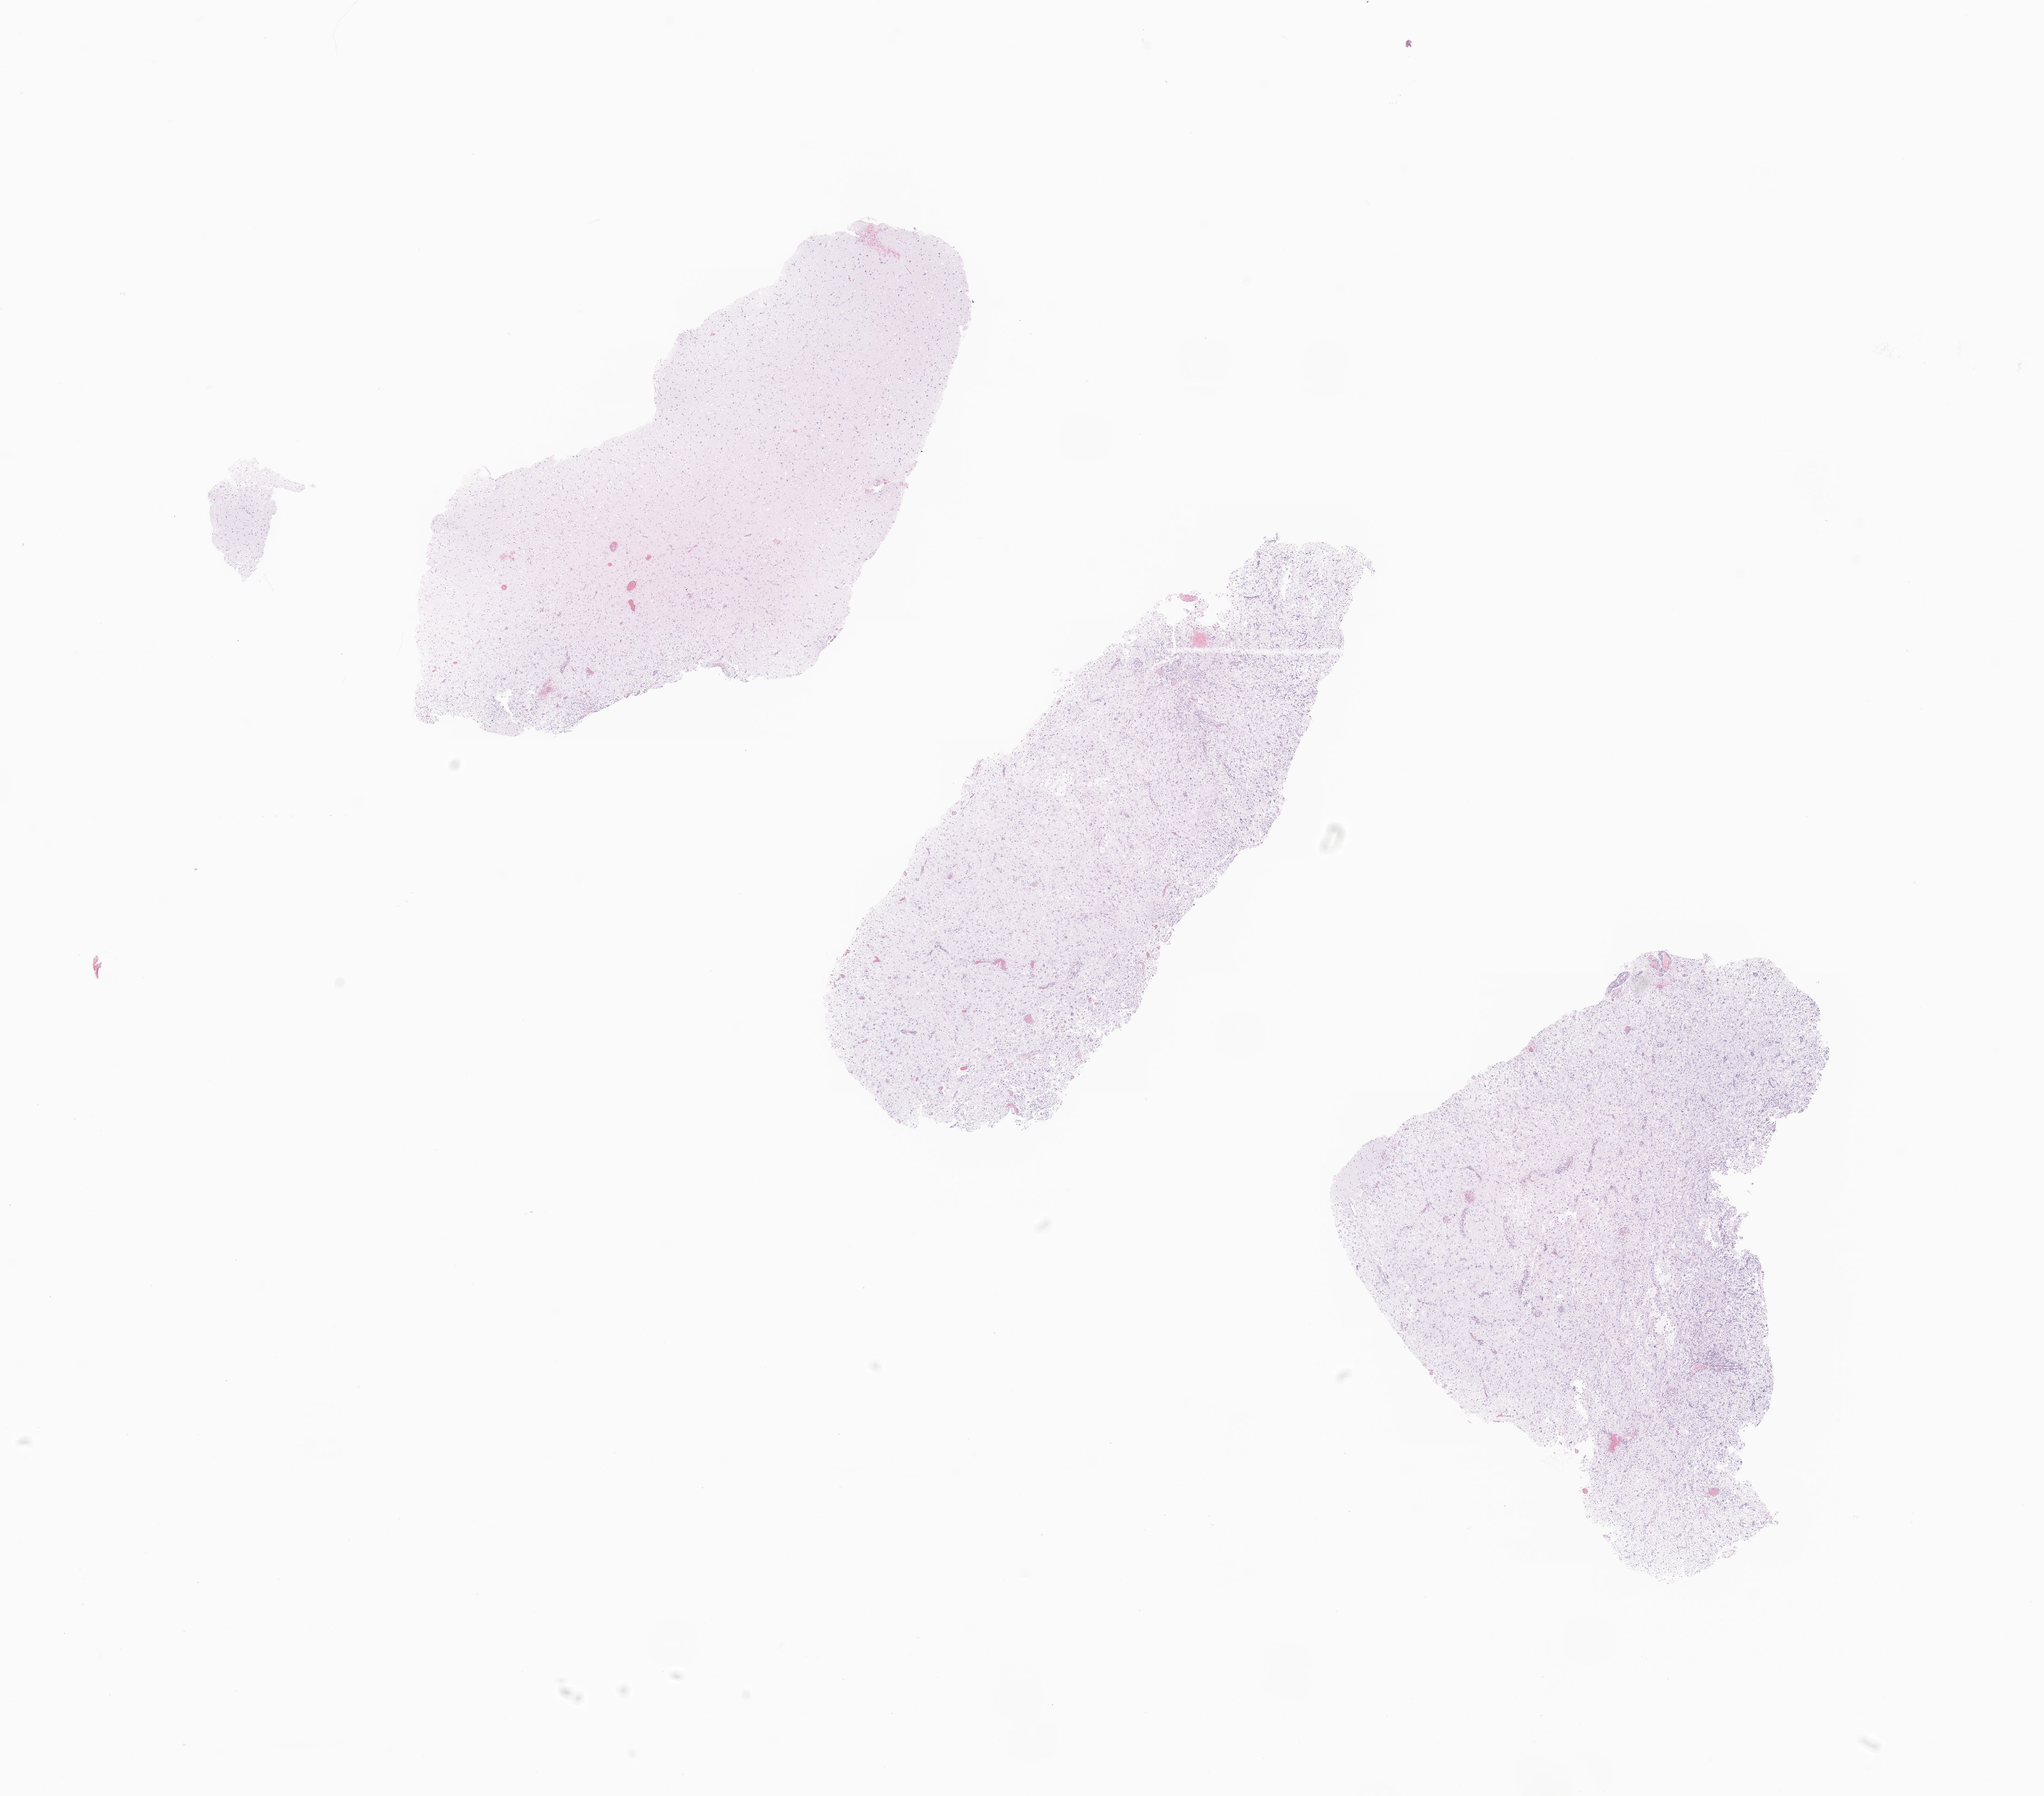
Digitized haematoxylin and eosin-stained section of tumor tissue from the brain, whole scanned area (about 18.6 x 16.3 mm) shown as a low-resolution overview, formalin-fixed, paraffin-embedded (FFPE) tissue. Male patient, age 101 months.
Recorded diagnosis: Ganglioglioma, NOS.